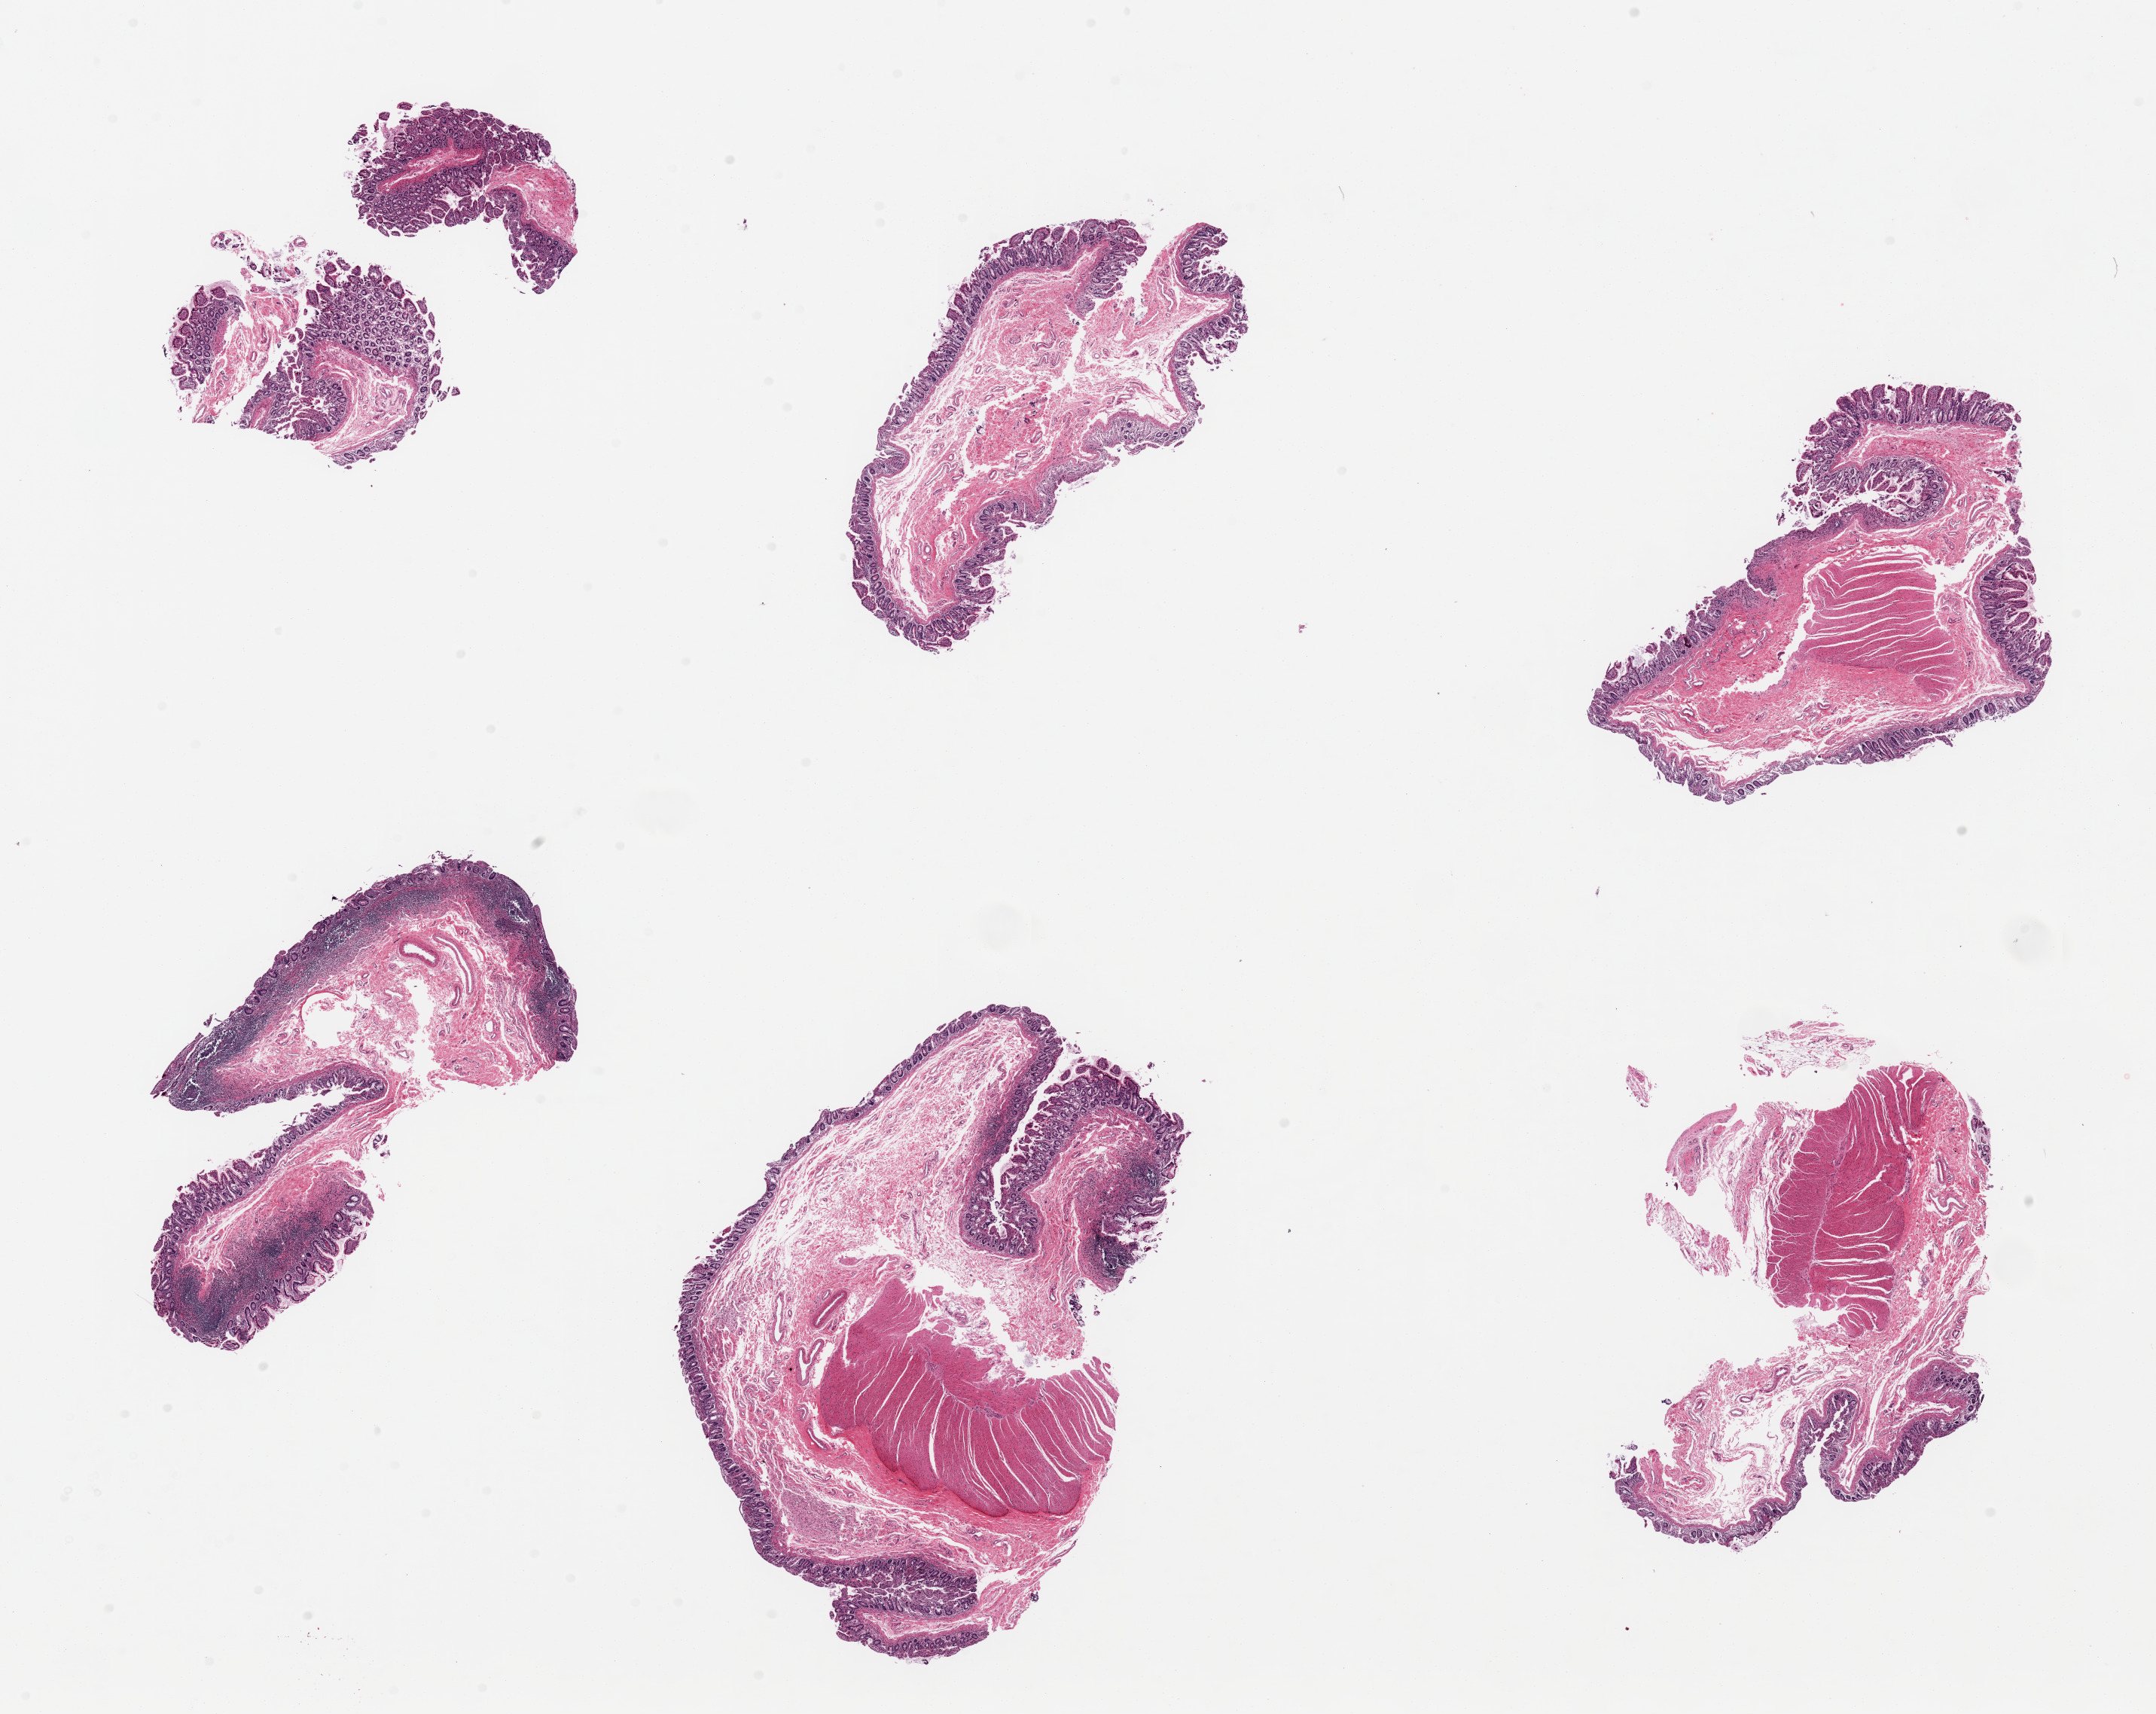
Whole-slide image, H&E stain — whole scanned area (about 22.6 x 18.0 mm, acquisition: 20x scan) shown as a low-resolution overview, PAXgene-fixed paraffin-embedded (PFPE) section, sampled site (target tissue): ileum, tissue donor sample. Donor: female.
Pathologist's review note for this sample: 6 pieces, target lymphoid aggregates are ~10% tissue, borderline.